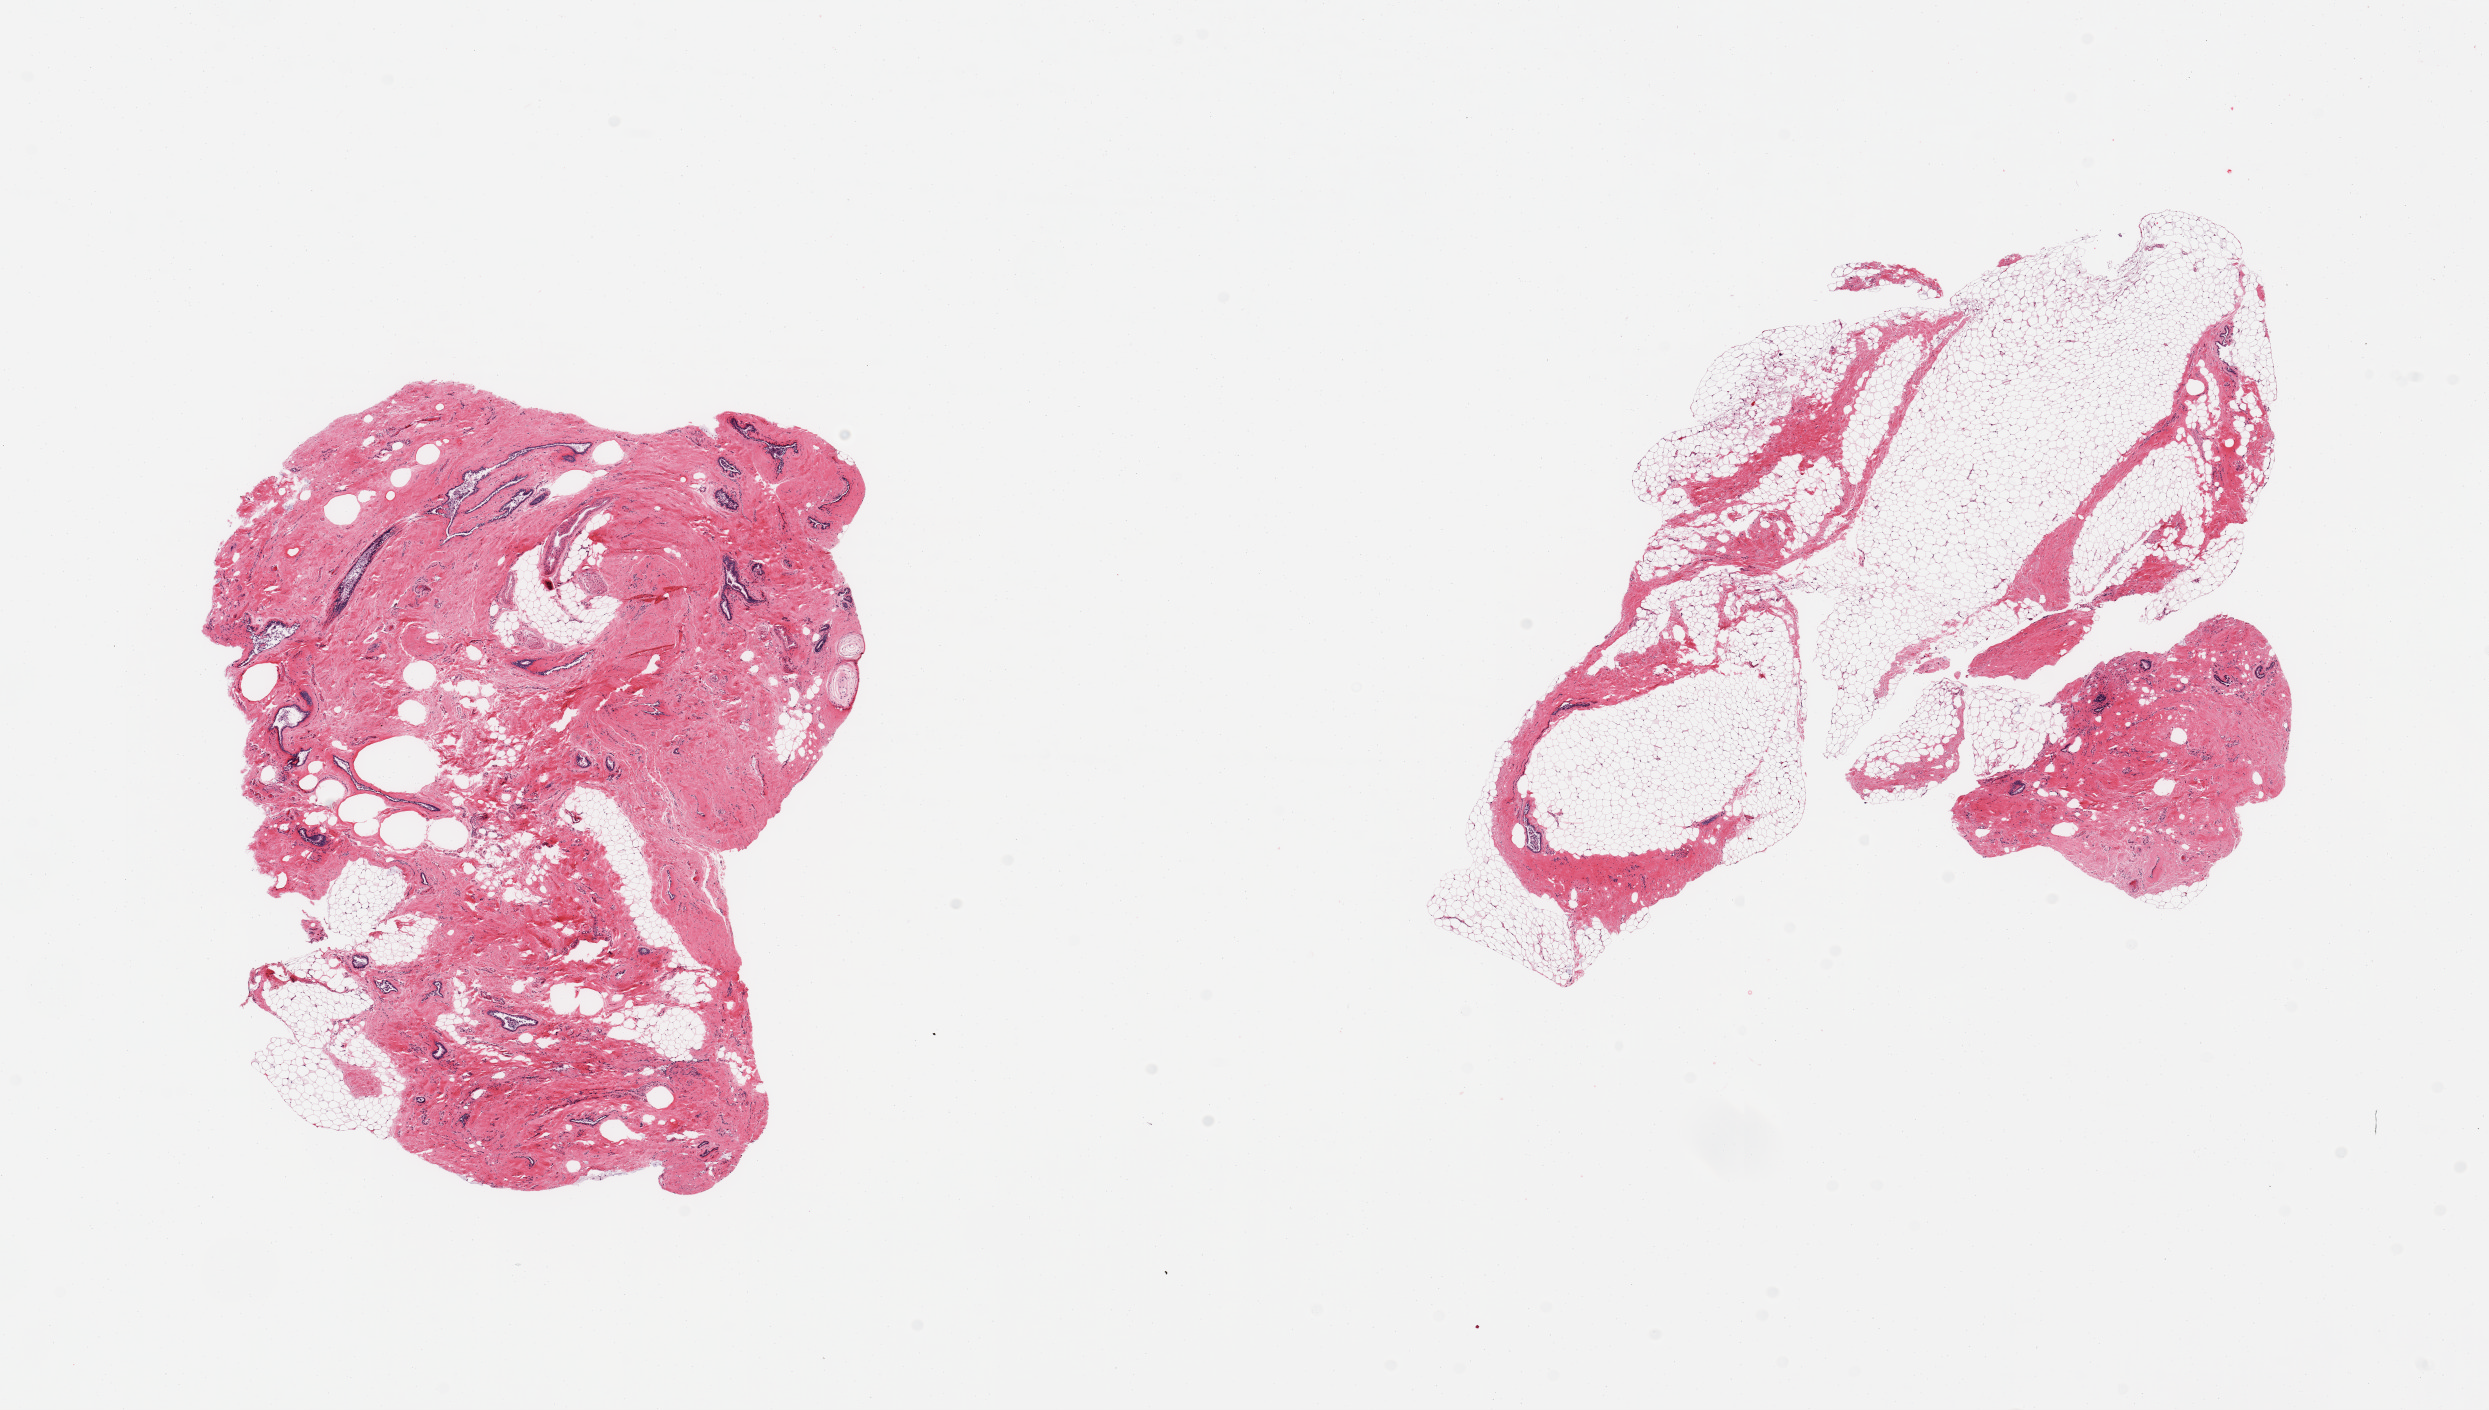
Hematoxylin and eosin (H&E) whole-slide image, brightfield, a low-resolution overview of the entire scanned area, about 19.7 x 11.2 mm. PAXgene-fixed paraffin-embedded (PFPE) section. Target tissue: breast. Donor tissue sample. Male donor.
Reviewer comment on this tissue sample: 2 pieces, gynecomastoid stromal and ductal hyperlasia.